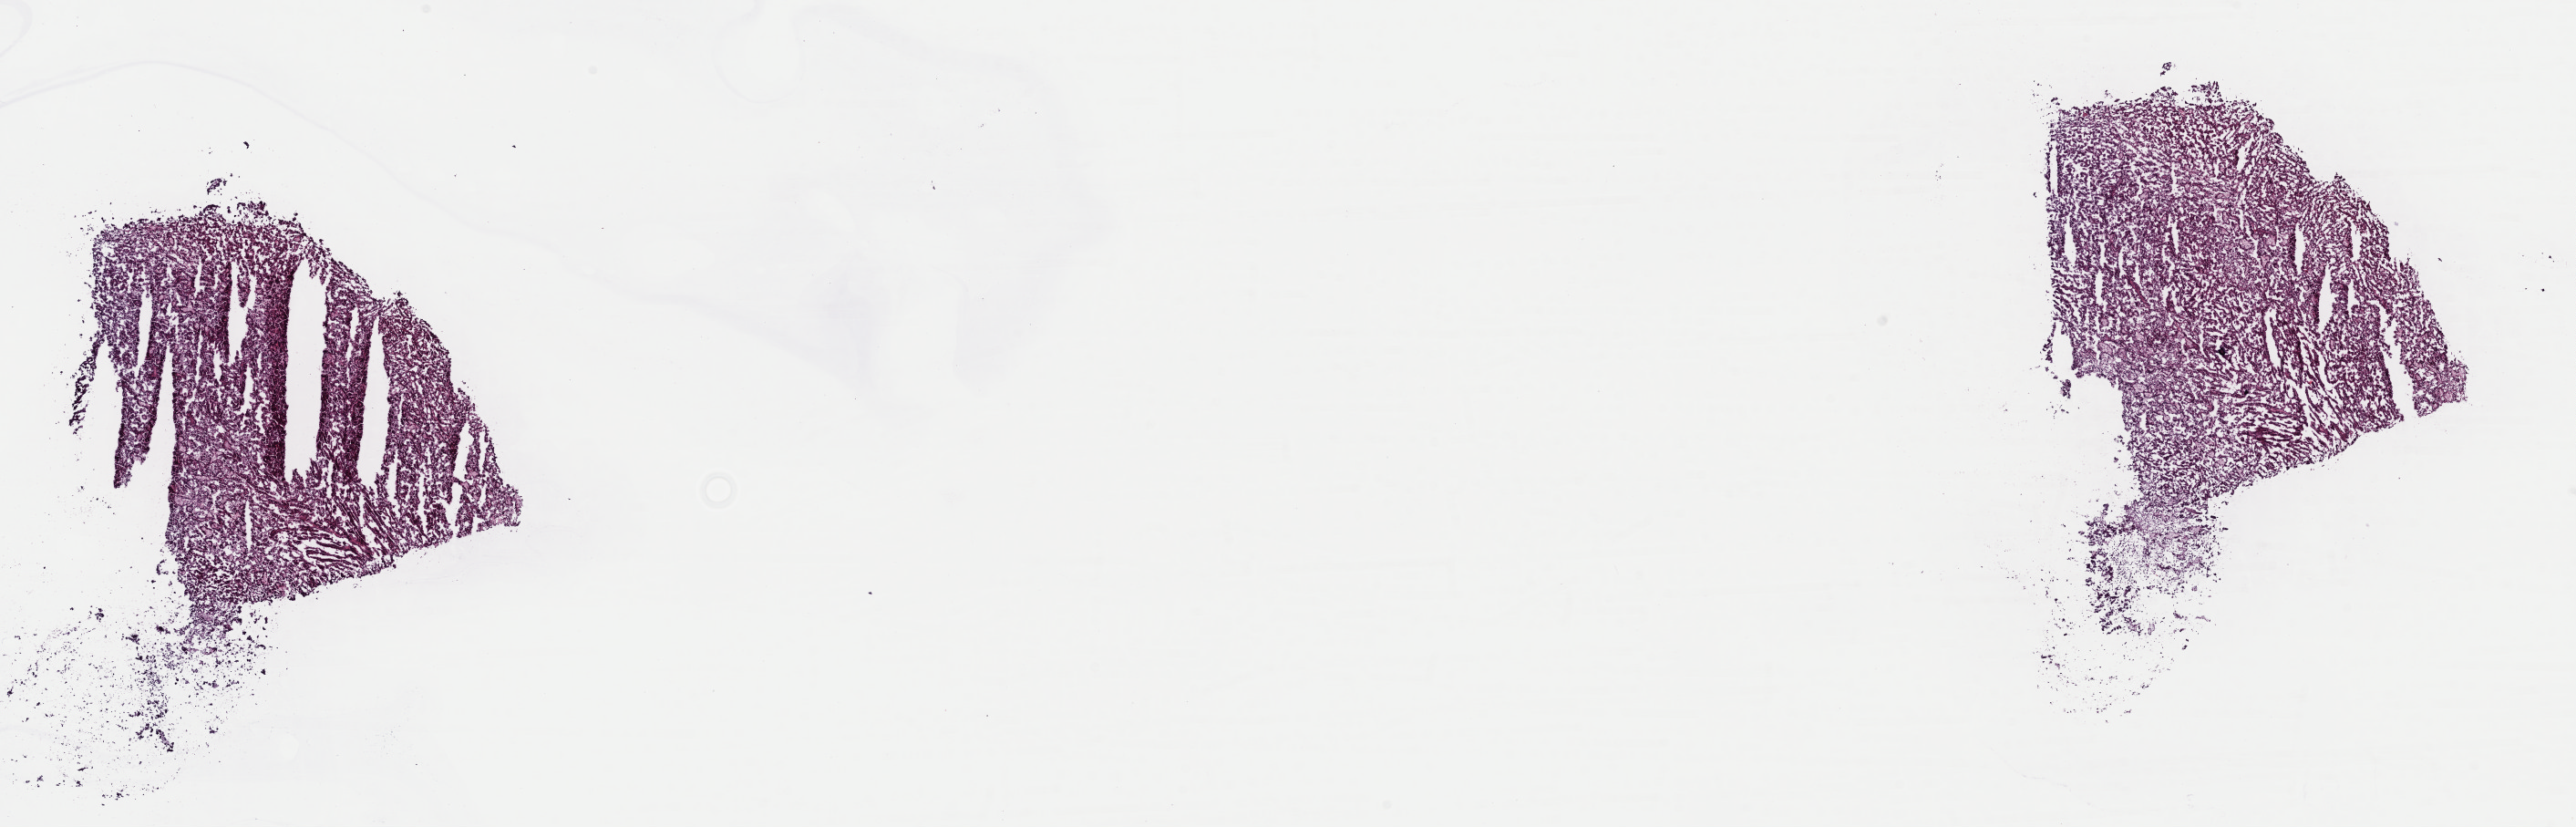
Digitized H&E tissue section (whole slide) — low-resolution overview of the scanned area, about 22.3 x 7.2 mm, frozen section from the top of the tissue portion, kidney, primary tumour sample. Female, age 45 years at initial diagnosis. Slide review estimates, as recorded: tumour cells 100%, tumour nuclei 80%.
Diagnosis: Papillary adenocarcinoma, NOS.